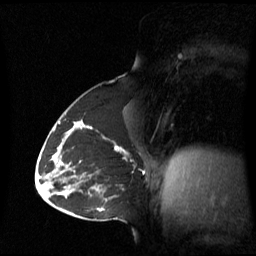
Breast MRI (dynamic contrast-enhanced), one sagittal slice; position 34 of 60 along the scan axis; dynamic contrast-enhanced series, image 2 of 3 at this slice position (ordered by acquisition); 1.5 T; TE 4.2 ms, TR 8.4 ms; 256 × 256 image matrix, field of view 270 × 270 mm. Patient: female, 43 years. Case-level facts recorded for this patient, not image findings: setting: breast cancer imaged before/during neoadjuvant chemotherapy; receptor status: triple-negative.
Structures marked on this image (semi-automatic segmentation, software-assisted and operator-edited):
- analysis volume of interest (the breast-tissue region the enhancement analysis was run in; not a lesion): bounding box [x1, y1, x2, y2] px = [62, 124, 135, 180]
- tumour enhancement mask (voxels above the 70 % enhancement threshold inside the analysis volume of interest): [80, 124, 125, 152]